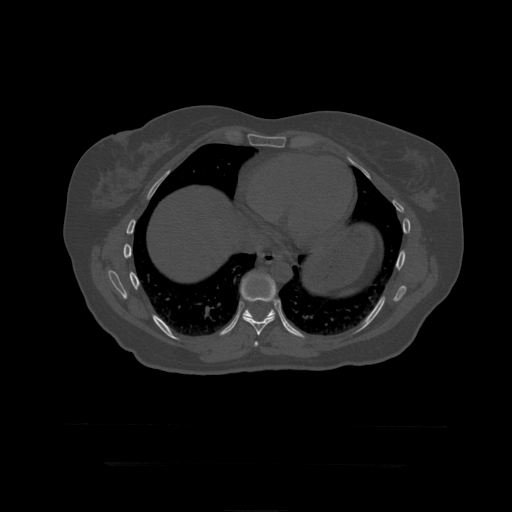
CT including the spine, one axial slice. Slice 255 of 399 in the series (ordered by position). Reconstruction kernel STANDARD. Bone window (W 1800 / L 400 HU). 1.25 mm slice thickness. 512 × 512 image matrix. Patient age 41 years. Case-level facts recorded for this patient, not image findings: primary cancer: breast.
Structures marked on this image (semi-automatic segmentation, software-assisted and operator-edited):
- T10 vertebra: bounding box <241,273,287,330> (left, top, right, bottom; pixels)
- T8 vertebra: <254,341,259,347>
- T9 vertebra: <241,274,278,336>